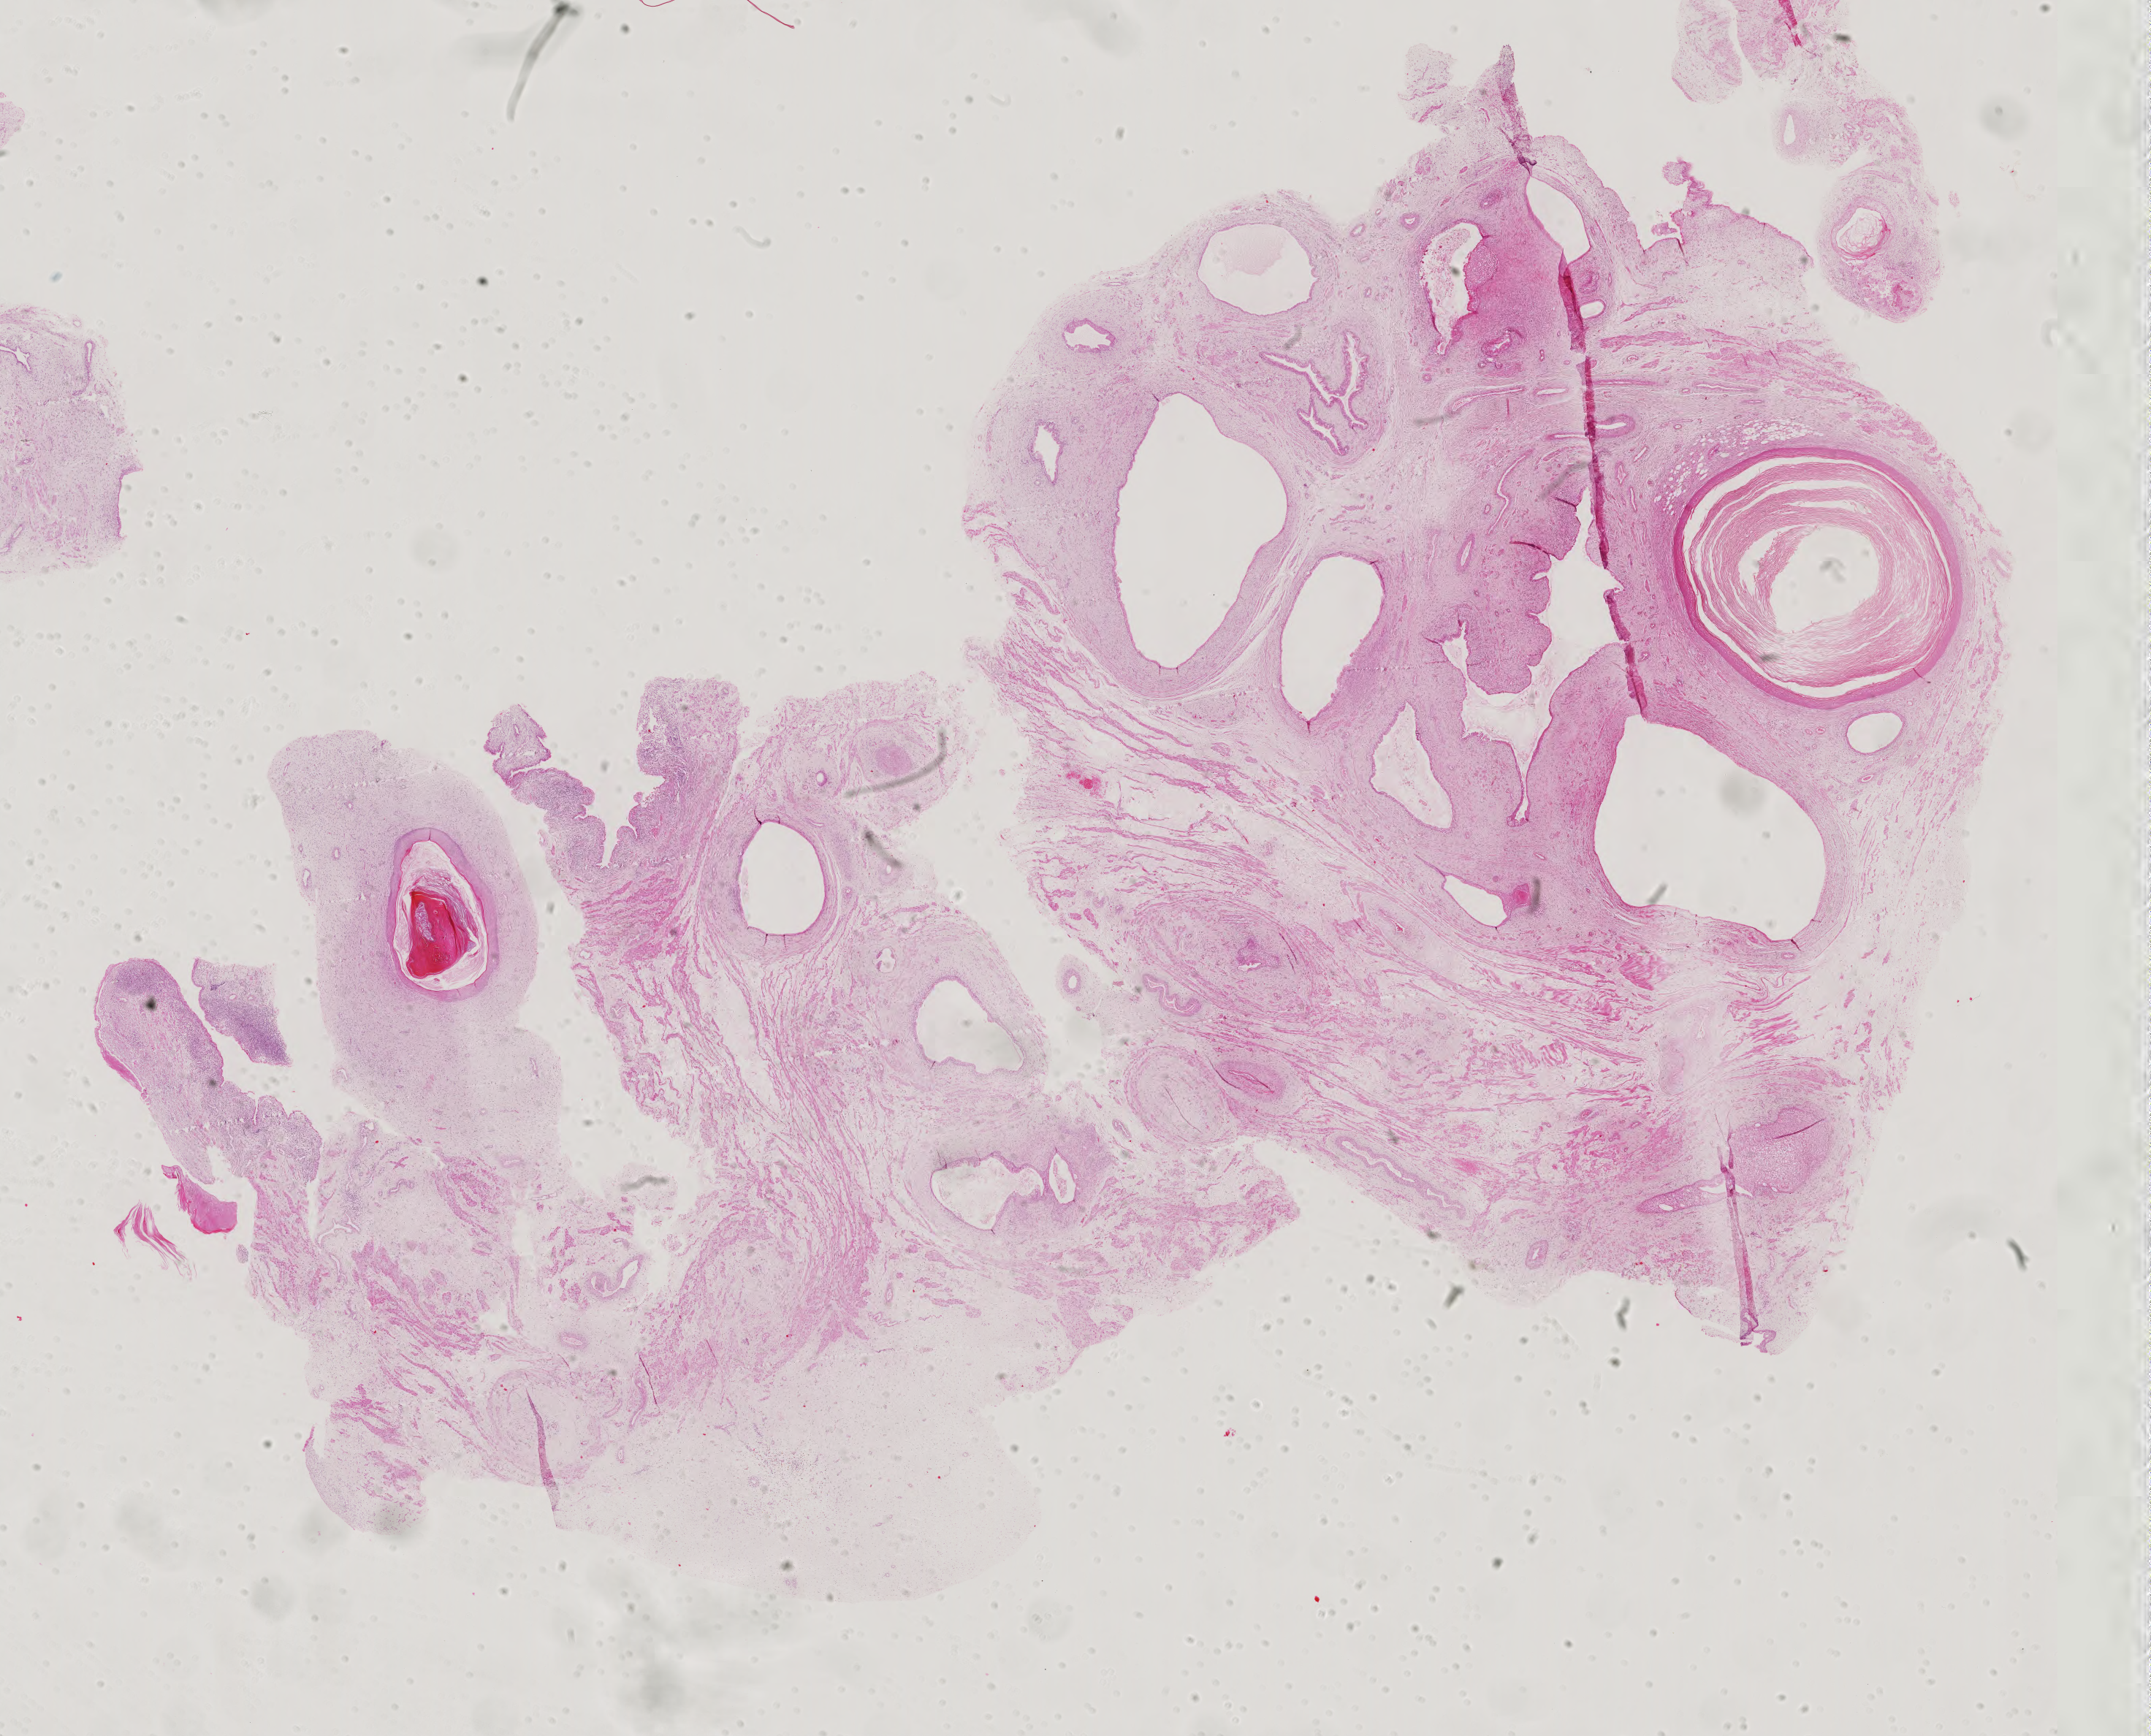
Digitized H&E tissue section (whole slide), a low-resolution overview of the entire scanned area, about 21.5 x 17.3 mm (from a 40x scan). Formalin-fixed paraffin-embedded (FFPE) diagnostic section. Primary tumour sample from the testis. Male, age 23 years at initial diagnosis.
AJCC pathologic stage: II (5th edition). Diagnosis: Teratoma, benign. TNM: T1 NX M0.